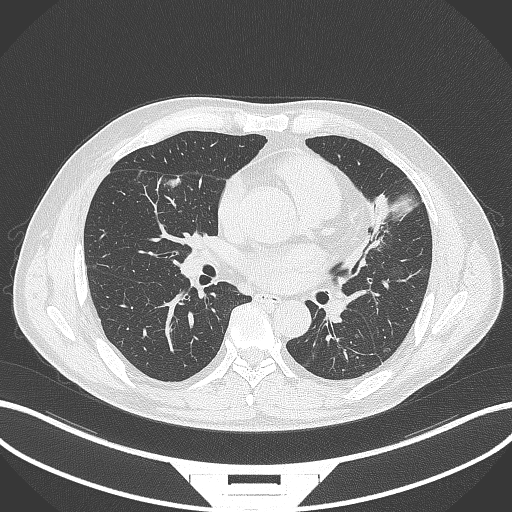
Chest CT, one axial slice; position 152 of 399 along the scan axis; reconstruction kernel B70f; lung window (W 1500 / L -600 HU); 1 mm slice thickness; 512 × 512 image matrix, field of view 400 × 400 mm. Patient: male, 59 years. Case-level facts recorded for this patient, not image findings: clinical TNM (as recorded): T2a N1 M0.
Annotated regions visible in this slice (rectangle marked by the reading radiologist):
- lung tumour (recorded histology: adenocarcinoma): bounding box (x1, y1, x2, y2) in pixels: (164, 163, 189, 194)